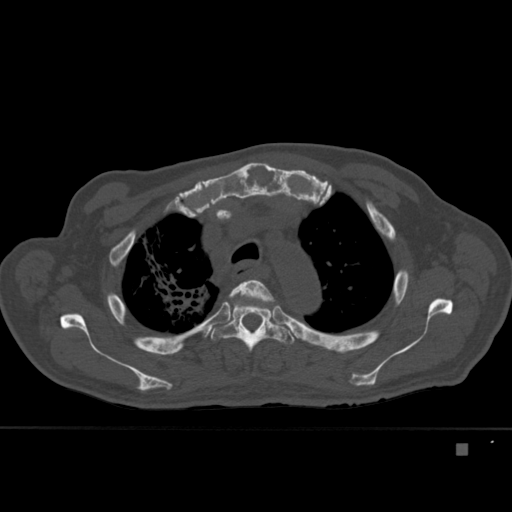
CT including the spine, one axial slice. Slice 325 of 451 in the series (ordered by position). Bone window (W 1800 / L 400 HU). 1.5 mm slice thickness. 512 × 512 image matrix, field of view 378 × 378 mm. Patient: male, 75 years. Case-level facts recorded for this patient, not image findings: primary cancer: prostate.
Structures marked on this image (semi-automatic segmentation, software-assisted and operator-edited):
- T3 vertebra: box from (x=229, y=280) to (x=275, y=303) px
- T4 vertebra: (x=210, y=299)–(x=295, y=353)